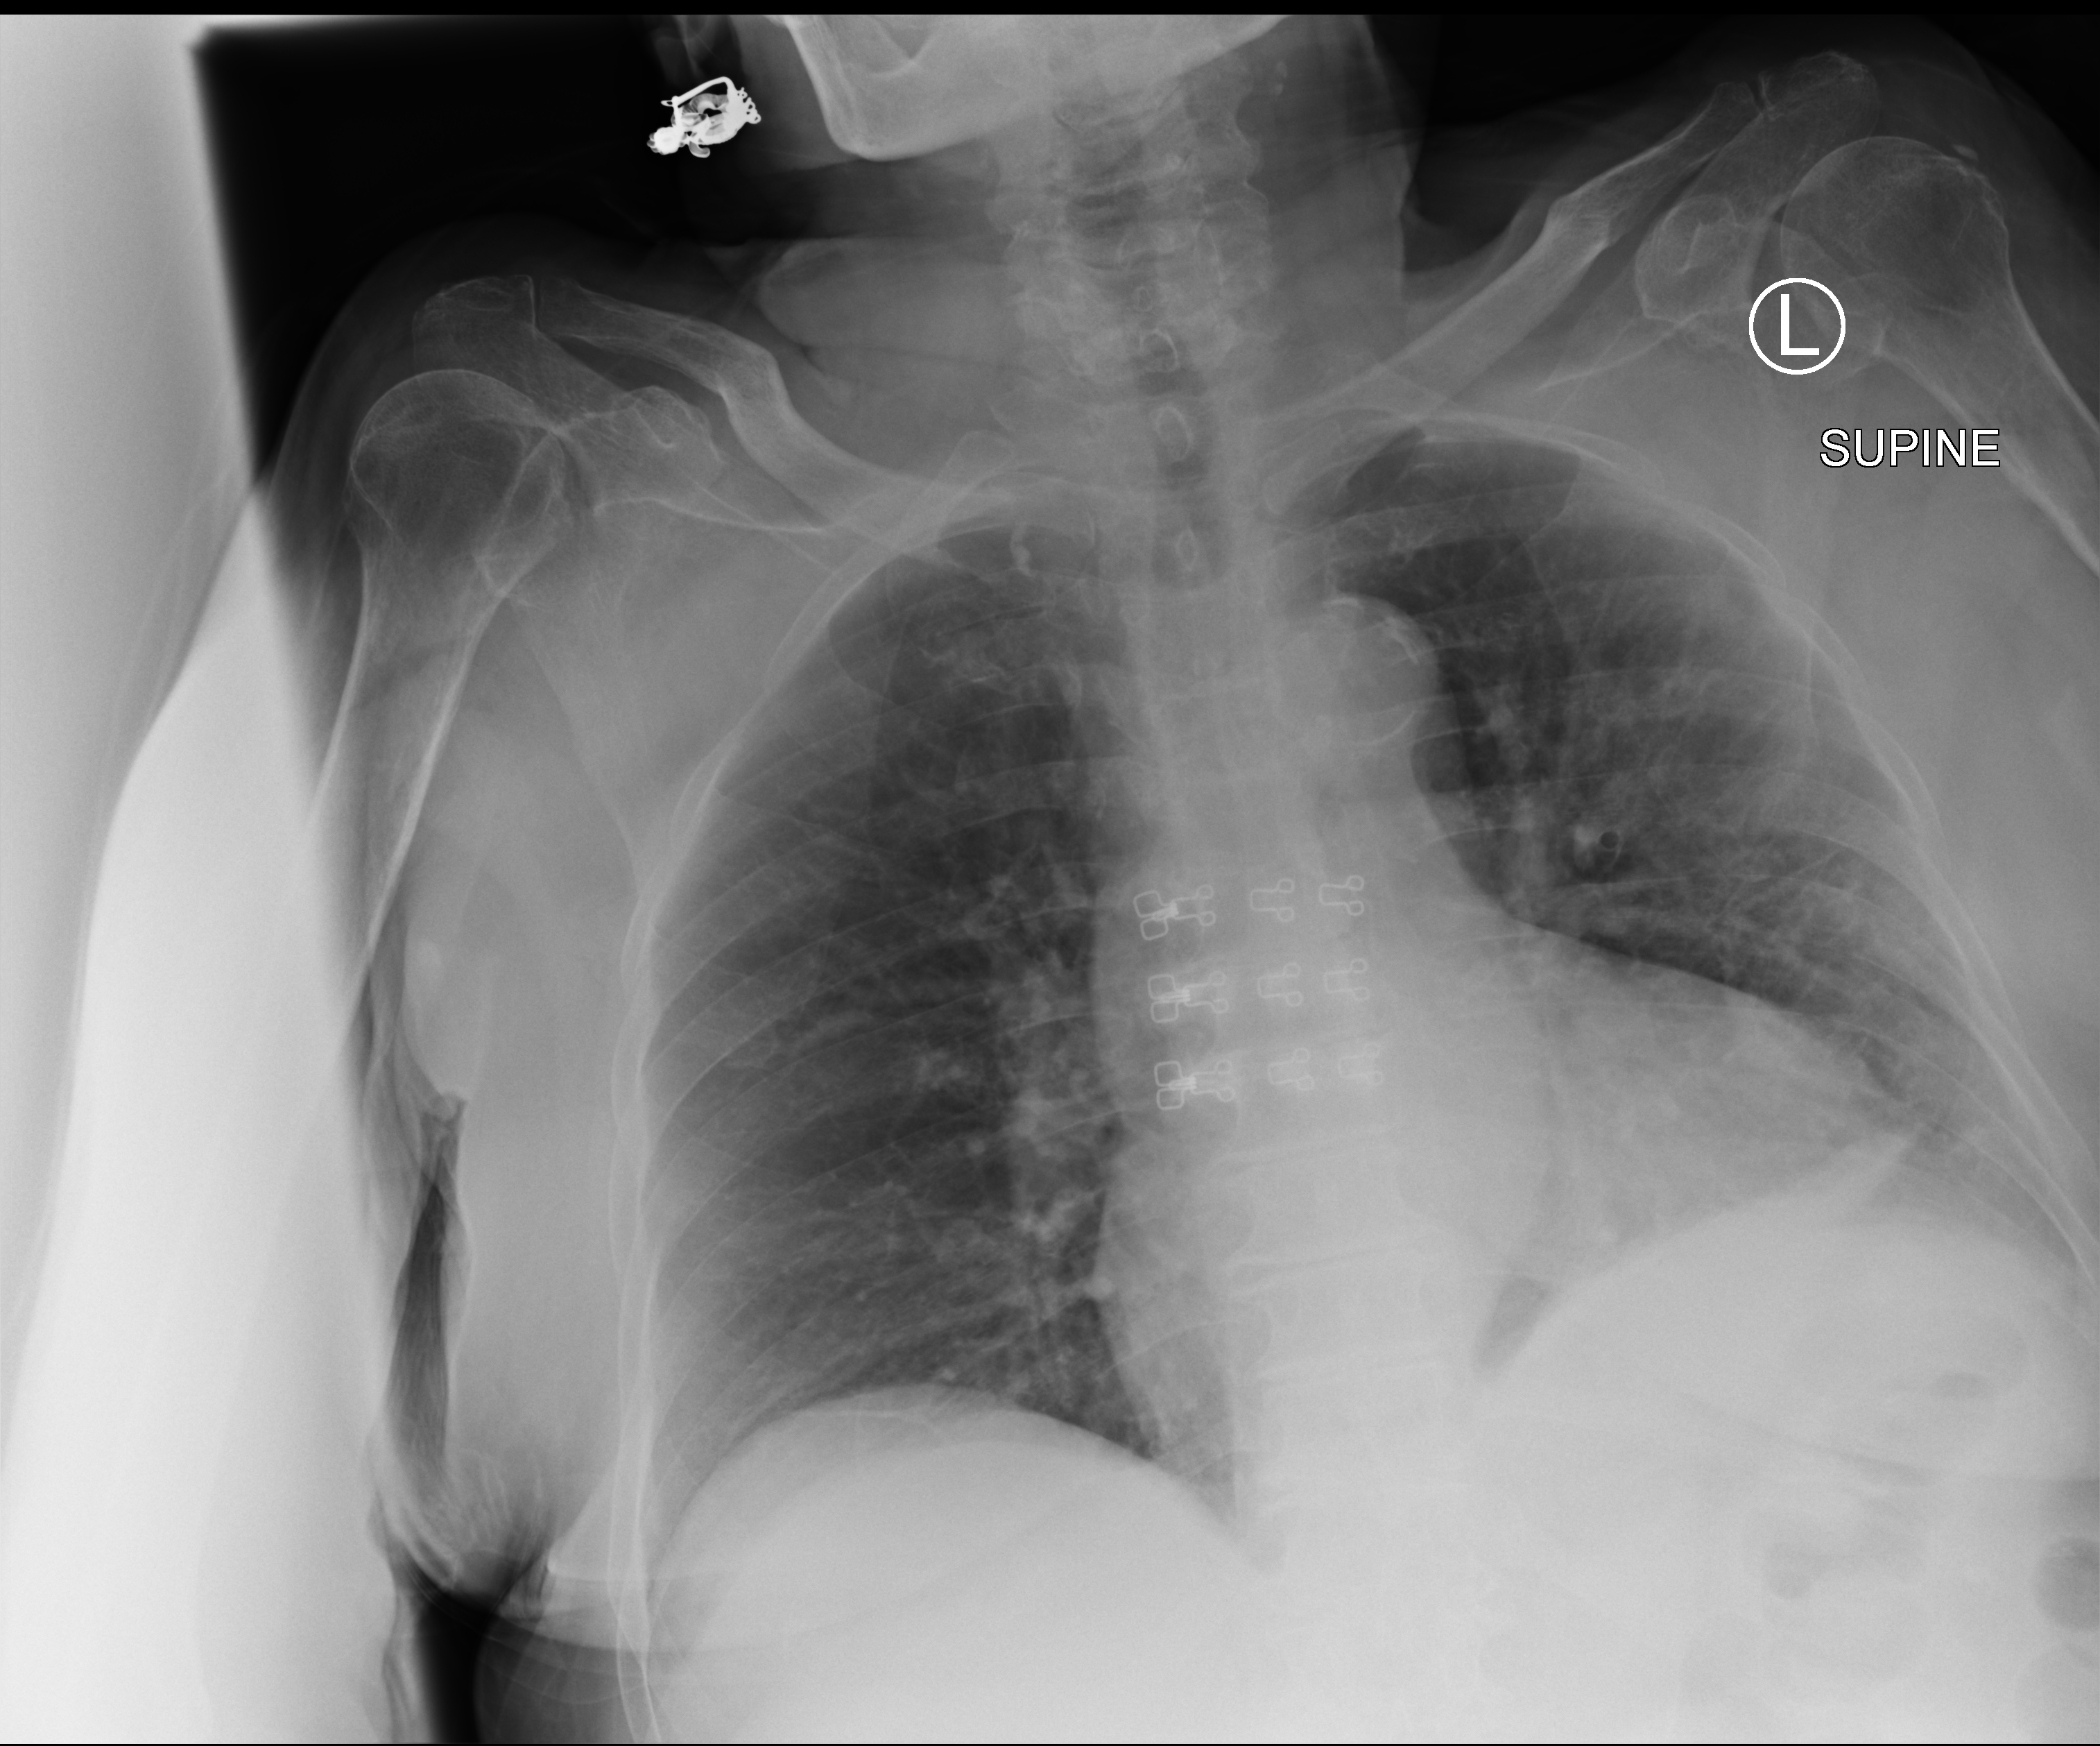
Chest X-ray (portable). Patient hospitalised with COVID-19; female, aged 75–90 years.
Hospital-stay facts (about this admission, not read from this image; timing relative to this image not recorded):
- other chronic lung disease (admission record): no